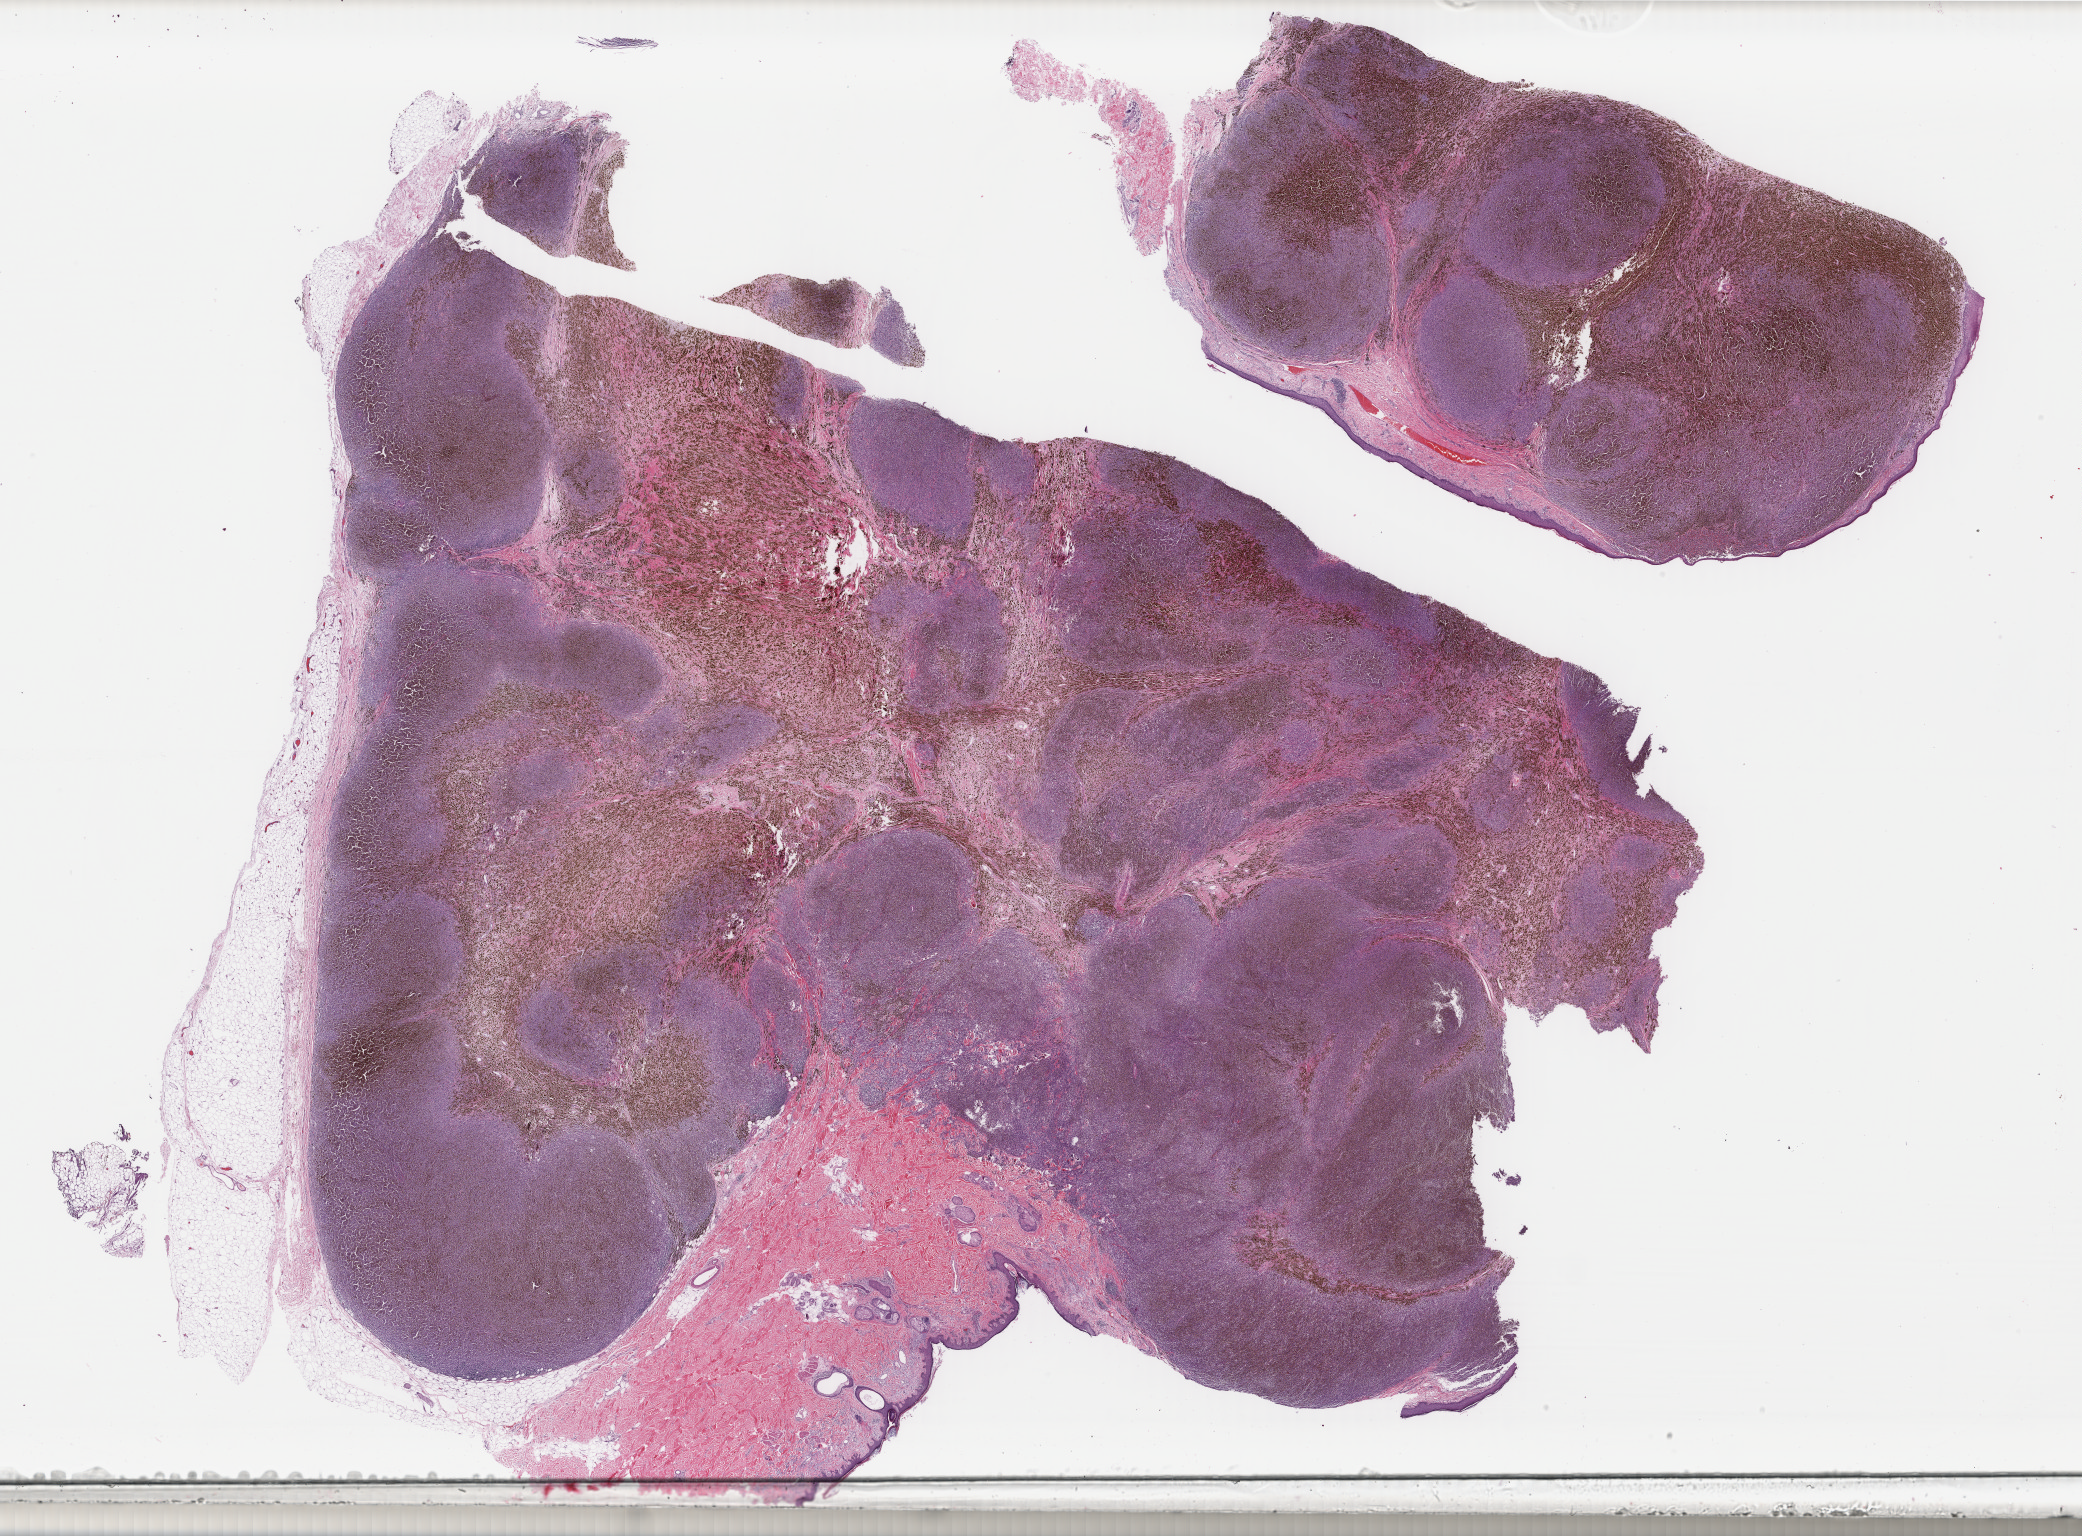
H&E-stained whole-slide image — low-resolution overview of the scanned area, about 33.1 x 24.4 mm (slide scanned at 40x). Formalin-fixed paraffin-embedded (FFPE) diagnostic section. Primary tumour sample from the skin. Patient: male, age at initial diagnosis 77 years.
Pathologic diagnosis: Malignant melanoma, NOS.